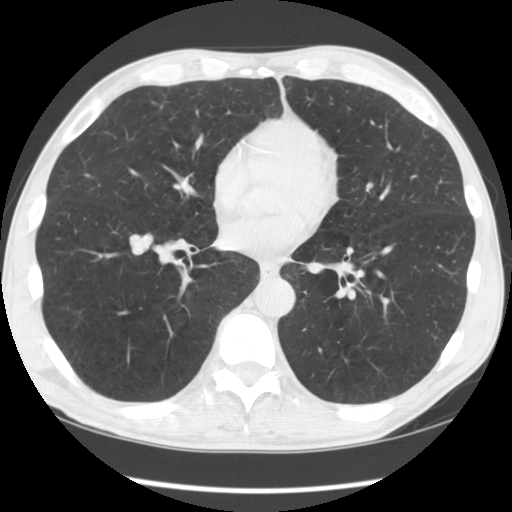
Low-dose screening chest CT, one axial slice. Slice 51 of 135 in the series (ordered by position). 120 kVp. Lung window (W 1500 / L -600 HU). 512 × 512 image matrix, field of view 360 × 360 mm.
Outlined on this slice (outlined manually by an expert reader):
- lesion 1 (tumor, lower lobe of right lung): bounding box <129,233,154,255> (left, top, right, bottom; pixels)